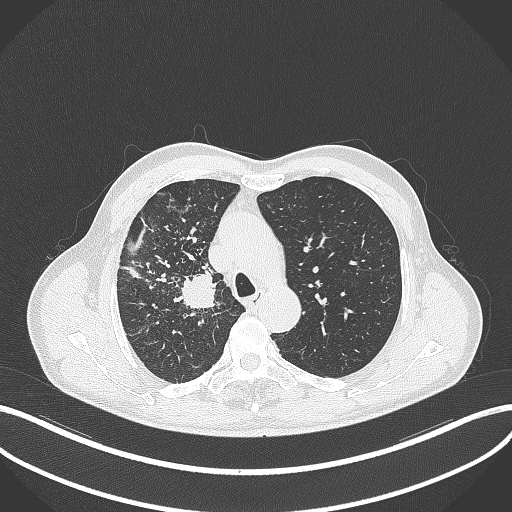
Chest CT, one axial slice. Position 349 of 490 along the scan axis. Reconstruction kernel B70f. 120 kVp. Lung window (W 1500 / L -600 HU). 1 mm slice thickness. 512 × 512 image matrix, field of view 400 × 400 mm. Male patient, age 69 years. Case-level facts recorded for this patient, not image findings: clinical TNM (as recorded): T2a N0 M0.
Annotated regions visible in this slice (rectangle marked by the reading radiologist):
- lung tumour (recorded histology: adenocarcinoma): box from (x=176, y=268) to (x=225, y=312) px